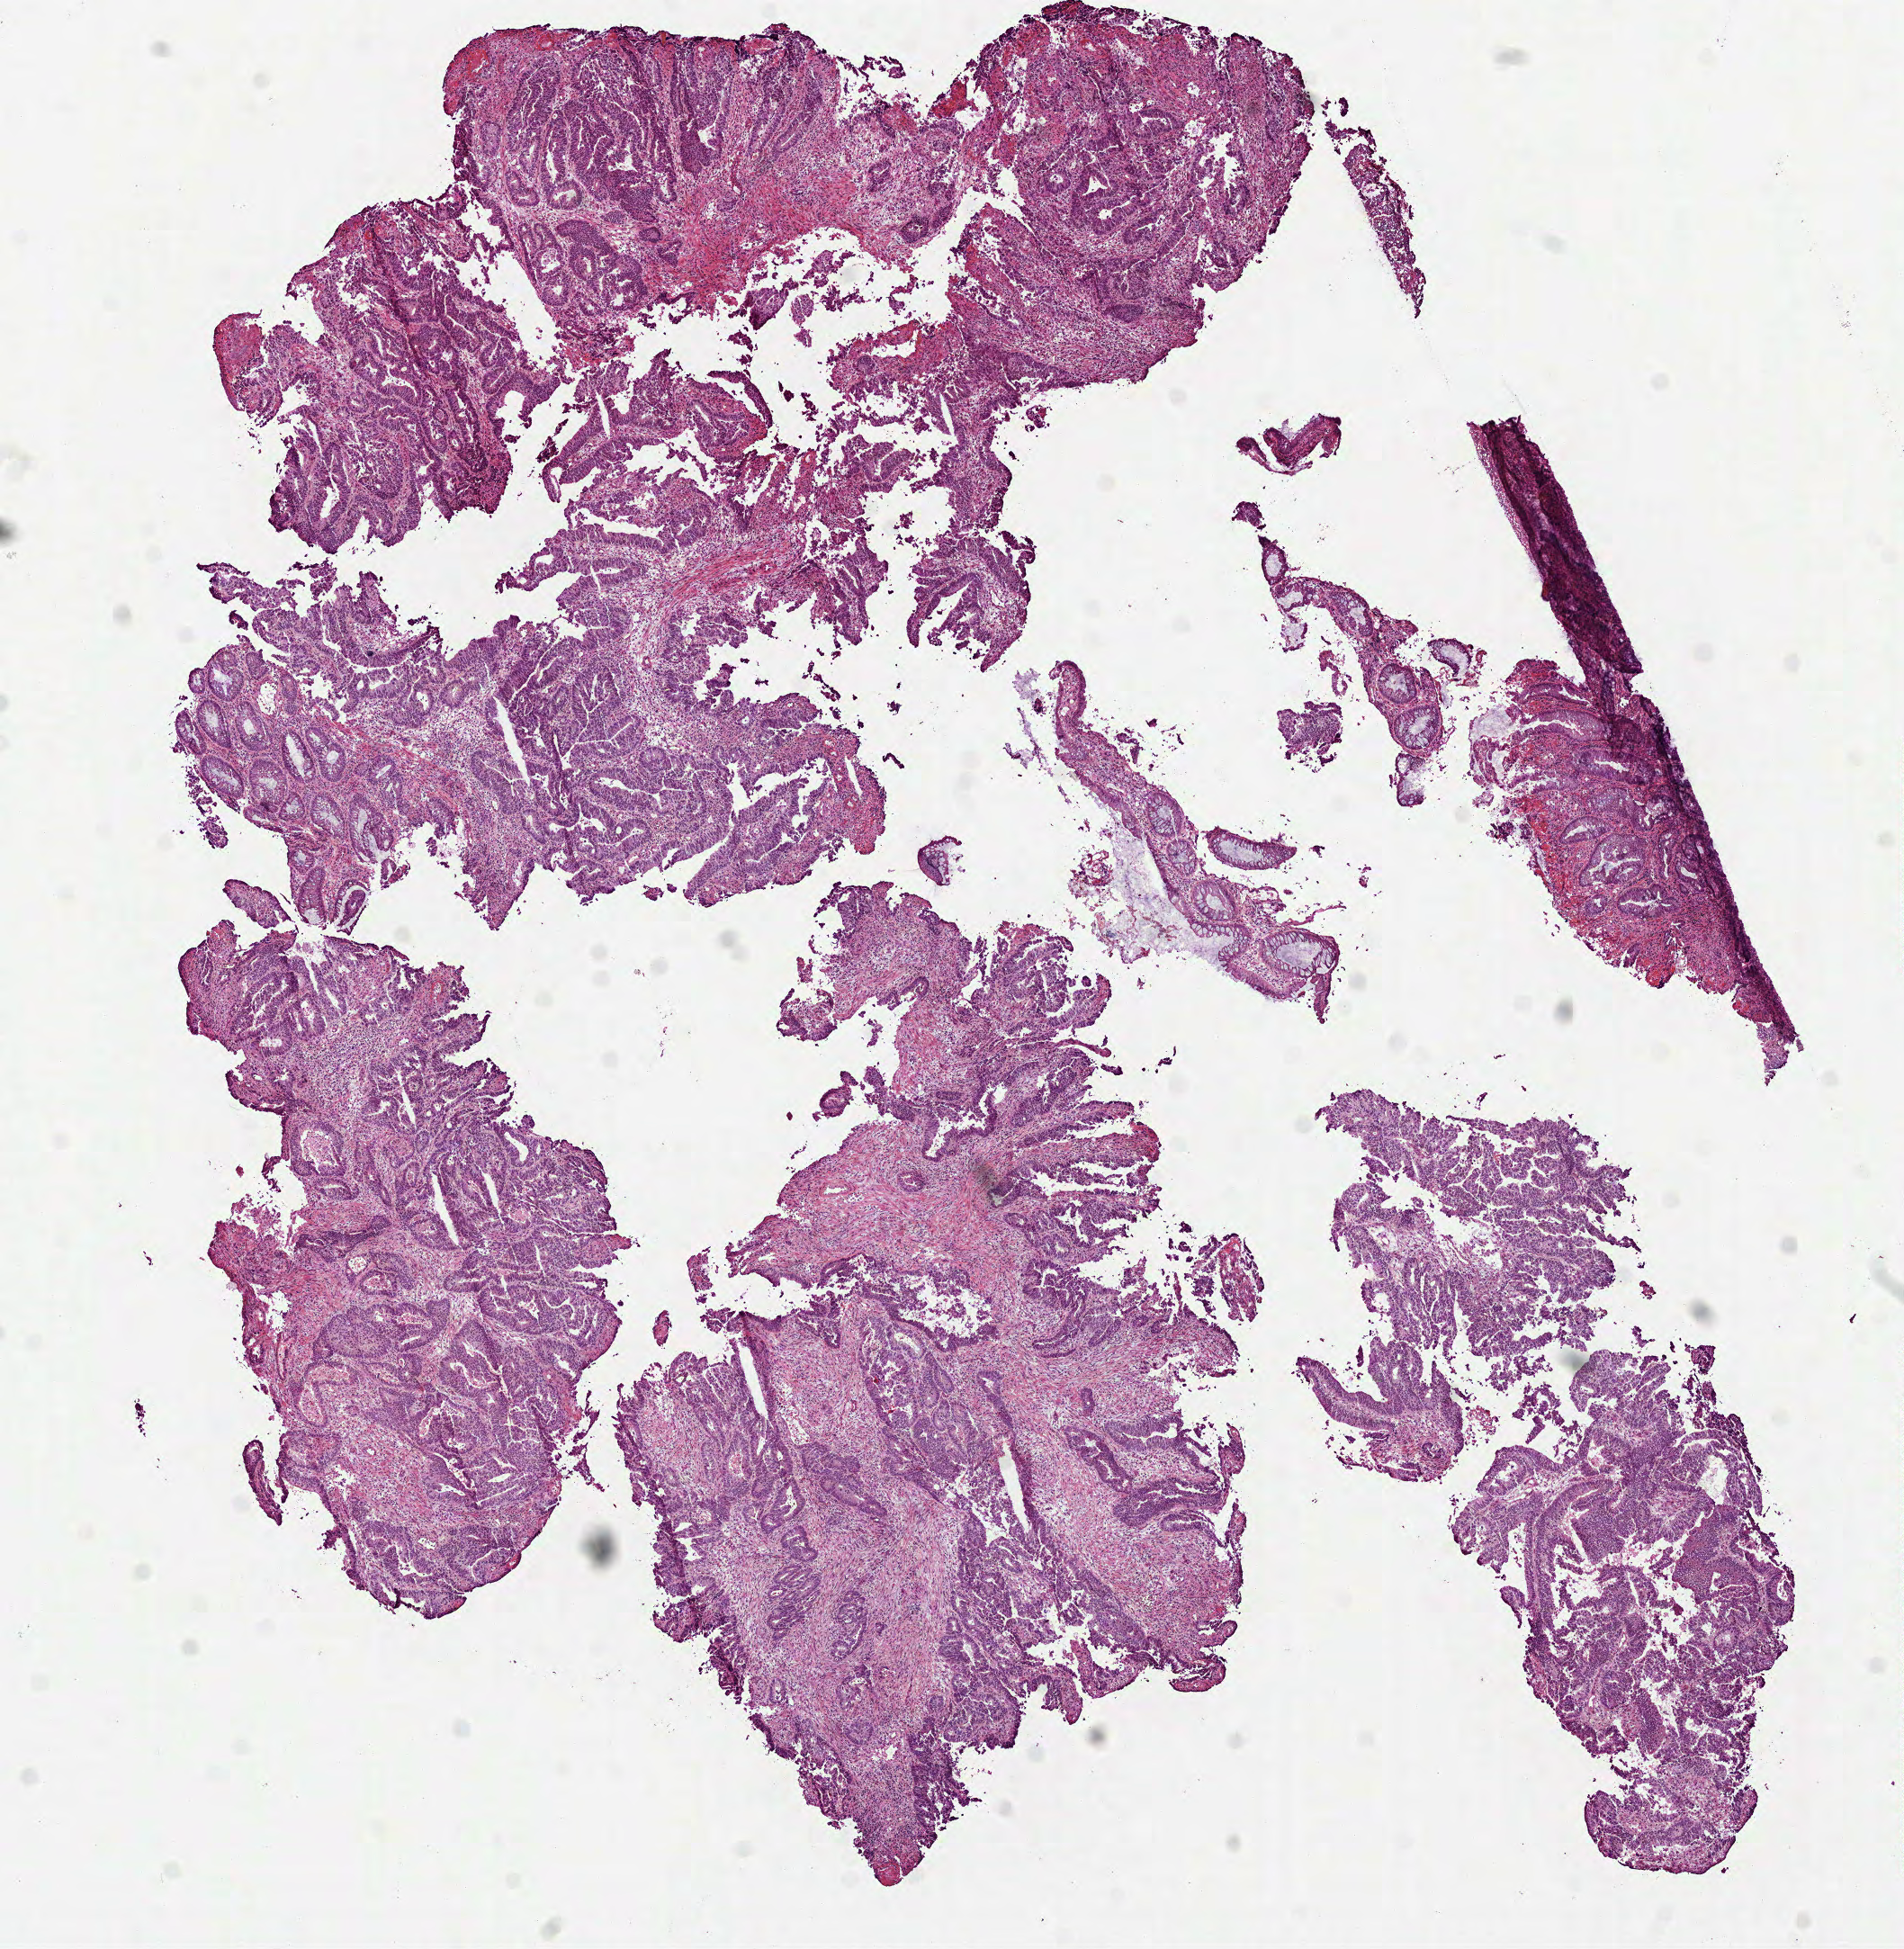
Whole-slide histology image, H&E-stained, low-resolution overview of the scanned area, about 8.5 x 8.7 mm; frozen section from the top of the tissue portion; primary tumour sample from the rectum. Male patient; age at initial diagnosis 63 years. Slide review estimates, as recorded: tumour cells 72%, tumour nuclei 65%, normal cells 10%, stromal cells 15%, necrosis 3%.
Lymph nodes positive (case pathology): 0 of 2 examined. Diagnosis: Adenocarcinoma, NOS. AJCC pathologic stage: IIIB (7th edition).